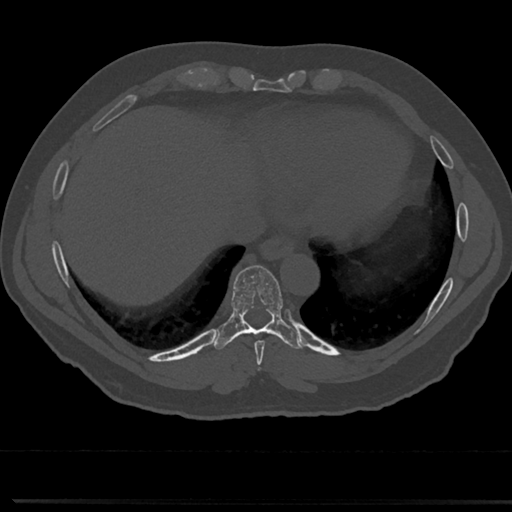
CT including the spine, one axial slice; position 315 of 817 along the scan axis; reconstruction kernel Br40s/3; bone window (W 1800 / L 400 HU); 512 × 512 image matrix, field of view 355 × 355 mm. Patient: male, 61 years. From the clinical record (not read from this slice): primary cancer: prostate.
Annotated regions visible in this slice (semi-automatically segmented with operator editing):
- T7 vertebra: bounding box <258,365,265,375> (left, top, right, bottom; pixels)
- T8 vertebra: <228,267,294,351>
- T9 vertebra: <236,324,280,327>